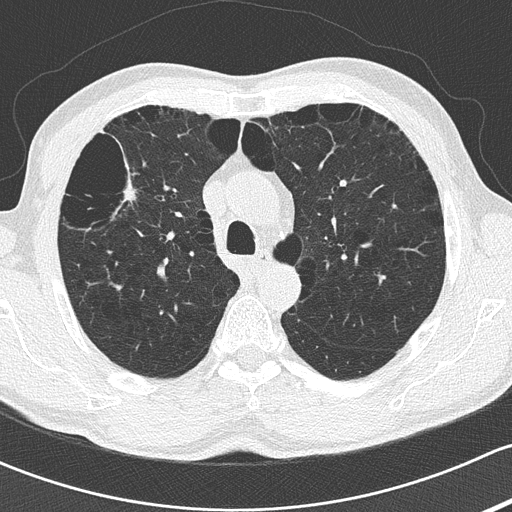
Axial slice from a low-dose chest CT screening exam; second screening round (one year after baseline); lung window (W 1500 / L -600 HU); 120 kVp. Male participant, aged 66 years at enrolment. Current smoker at enrolment.
Expert reader's lesion annotation, bounding box <97,157,156,215> (left, top, right, bottom; pixels). The screening reader recorded 3 non-calcified nodules or masses ≥4 mm on this exam; which of them this box marks is not recorded.